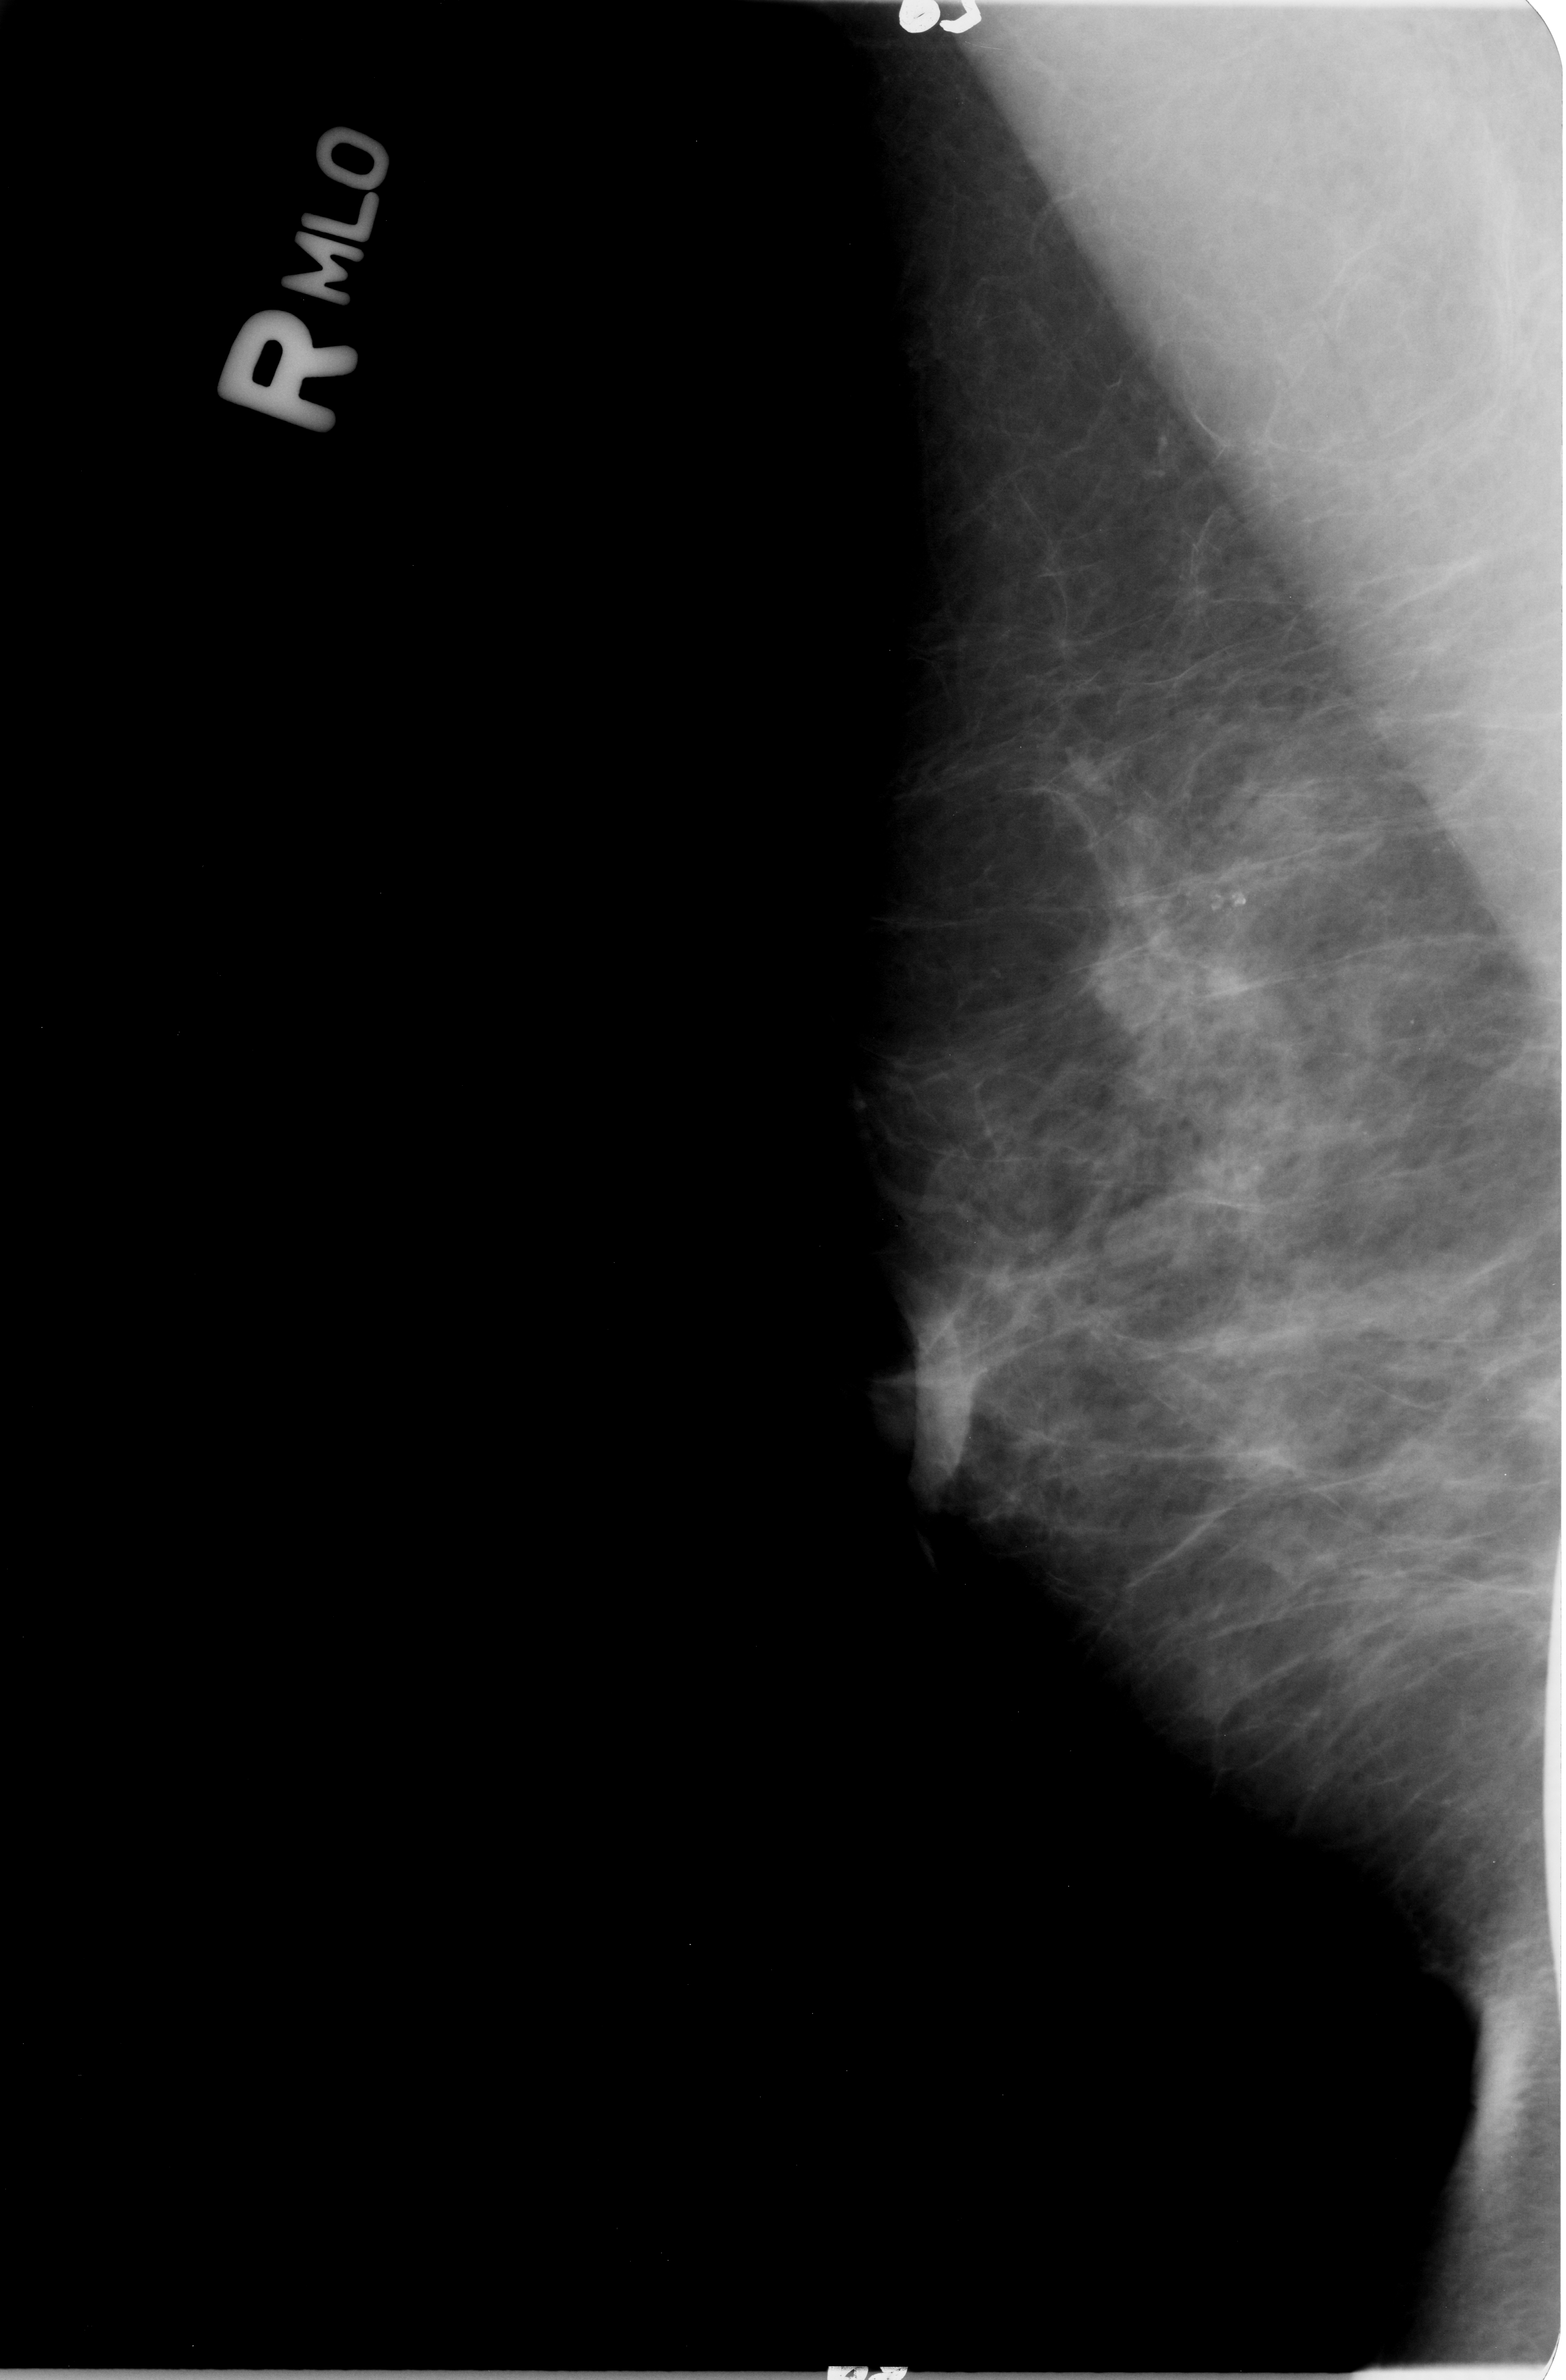
Scanned film-screen mammogram; right breast; MLO view; BI-RADS breast density category 3 (scale 1–4).
Radiologist-marked abnormalities on this image: Finding 1 of 2: mass, shape architectural distortion; BI-RADS assessment category 2; pathology (as recorded): benign. Finding 2 of 2: mass, shape architectural distortion; BI-RADS assessment category 2; subtlety rating 3 on a 1 (subtle) to 5 (obvious) scale; pathology result (as recorded, not read from the image): benign.